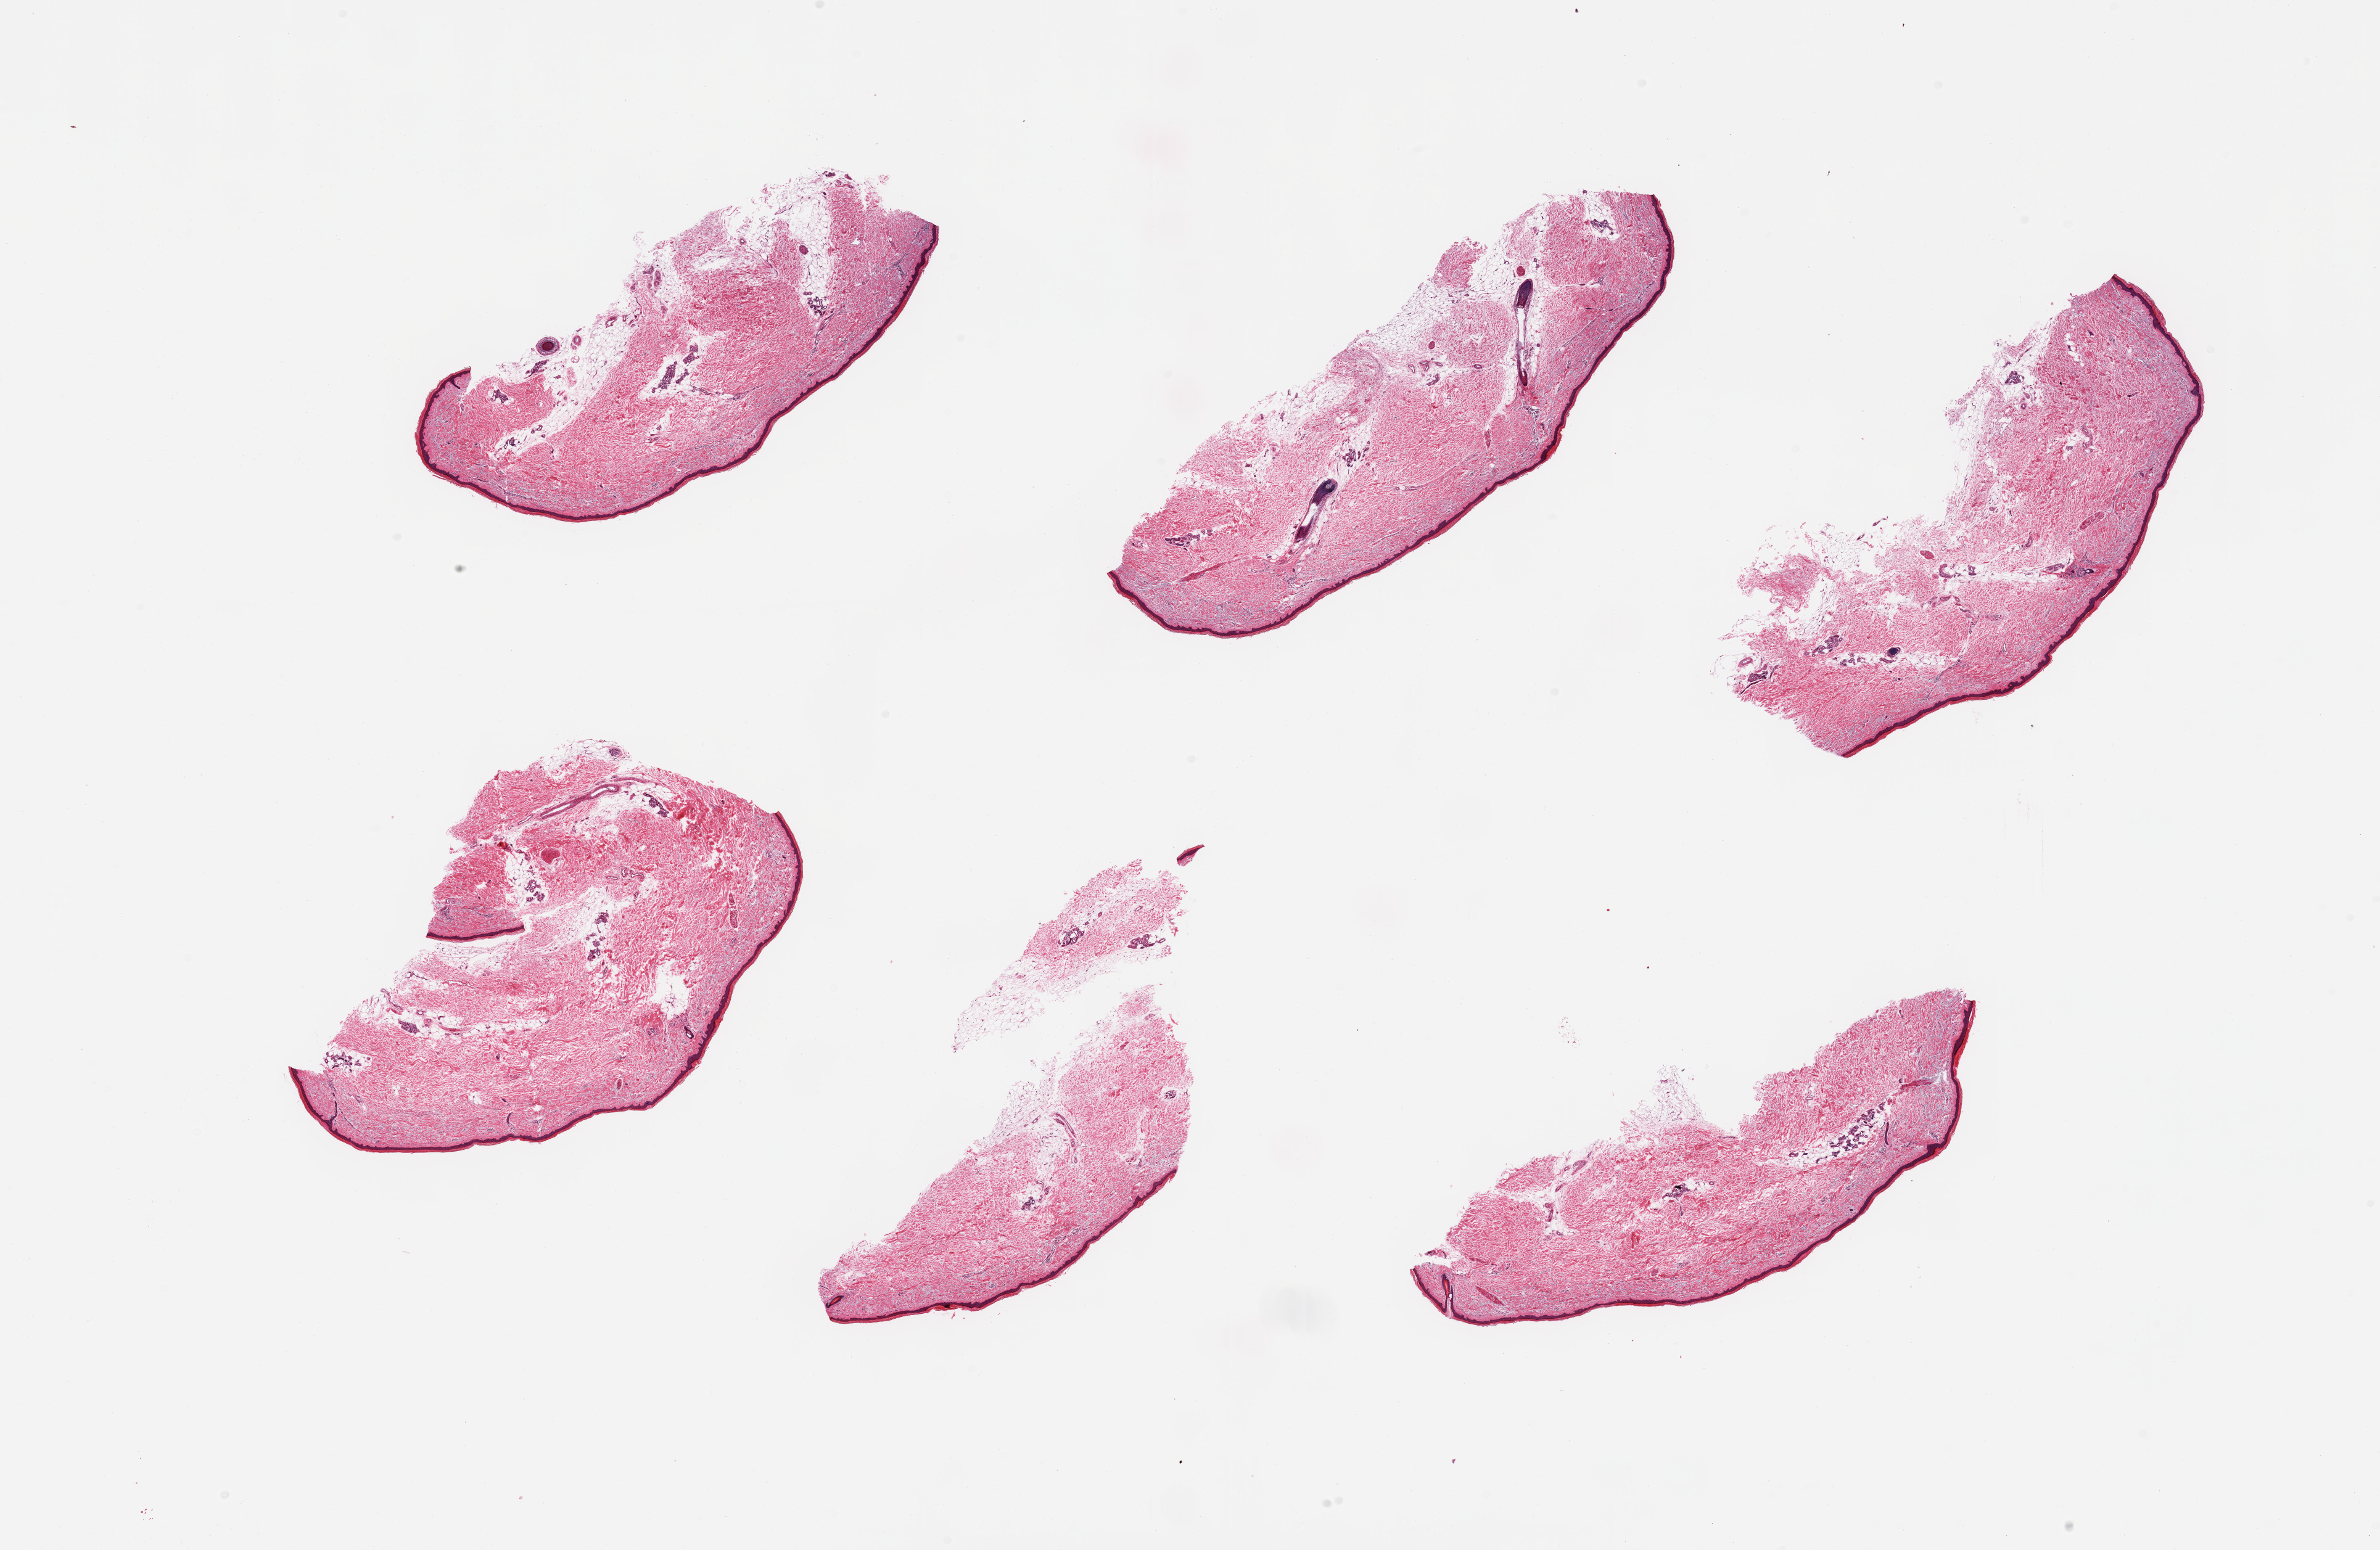
Haematoxylin and eosin whole-slide image, low-resolution overview of the scanned area, about 30.5 x 19.9 mm, PAXgene-fixed paraffin-embedded (PFPE) section, target tissue: skin of lower leg, tissue donor sample. Female donor.
Reviewer comment on this tissue sample: 6 pieces, moderate dermal fat; squamous epithelium is ~35-40 microns.